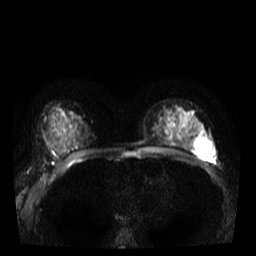
Breast MRI, one axial slice; position 22 of 40 along the scan axis; diffusion-weighted series; image 2 of 4 stored at this slice position (different b-values; order by instance number); 3 T; 5 mm slice thickness; 256 × 256 image matrix, field of view 320 × 320 mm. Female patient.
Annotated regions visible in this slice (outlined manually by an expert reader):
- tumour on diffusion-weighted imaging: box from (x=202, y=139) to (x=211, y=146) px